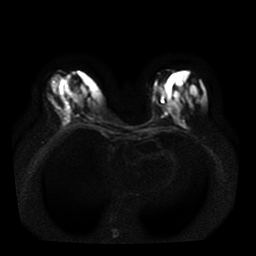
Breast MRI, one axial slice; slice 14 of 41 in the series (ordered by position); diffusion-weighted series; image 2 of 4 stored at this slice position (different b-values; order by instance number); 1.5 T; 256 × 256 image matrix, field of view 330 × 330 mm. Female patient.
Annotated regions visible in this slice (outlined manually by an expert reader):
- tumour on diffusion-weighted imaging: bounding box (x1, y1, x2, y2) in pixels: (67, 90, 73, 95)